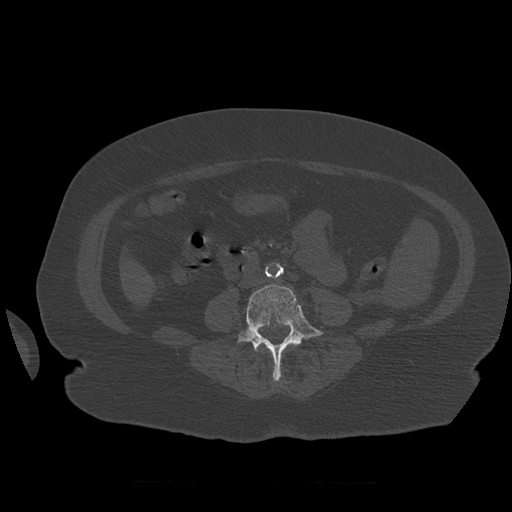
CT including the spine, one axial slice; position 207 of 399 along the scan axis; 120 kVp; bone window (W 1800 / L 400 HU); 512 × 512 image matrix. Patient age 81 years. Case-level facts recorded for this patient, not image findings: primary cancer: renal.
Structures marked on this image (semi-automatically segmented with operator editing):
- L4 vertebra: bounding box [x1, y1, x2, y2] px = [238, 284, 324, 381]